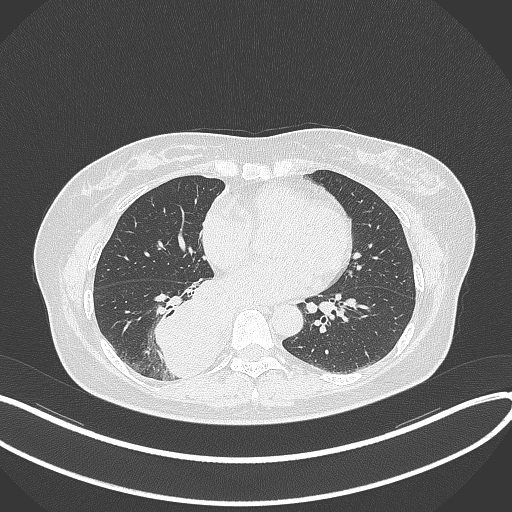
Chest CT, one axial slice; position 149 of 331 along the scan axis; reconstruction kernel B70f; lung window (W 1500 / L -600 HU); 512 × 512 image matrix, field of view 400 × 400 mm. Patient: female, 54 years. Case-level facts recorded for this patient, not image findings: clinical TNM (as recorded): T4 N0 M0.
Outlined on this slice (rectangle marked by the reading radiologist):
- lung tumour (recorded histology: adenocarcinoma): box from (x=150, y=280) to (x=234, y=381) px